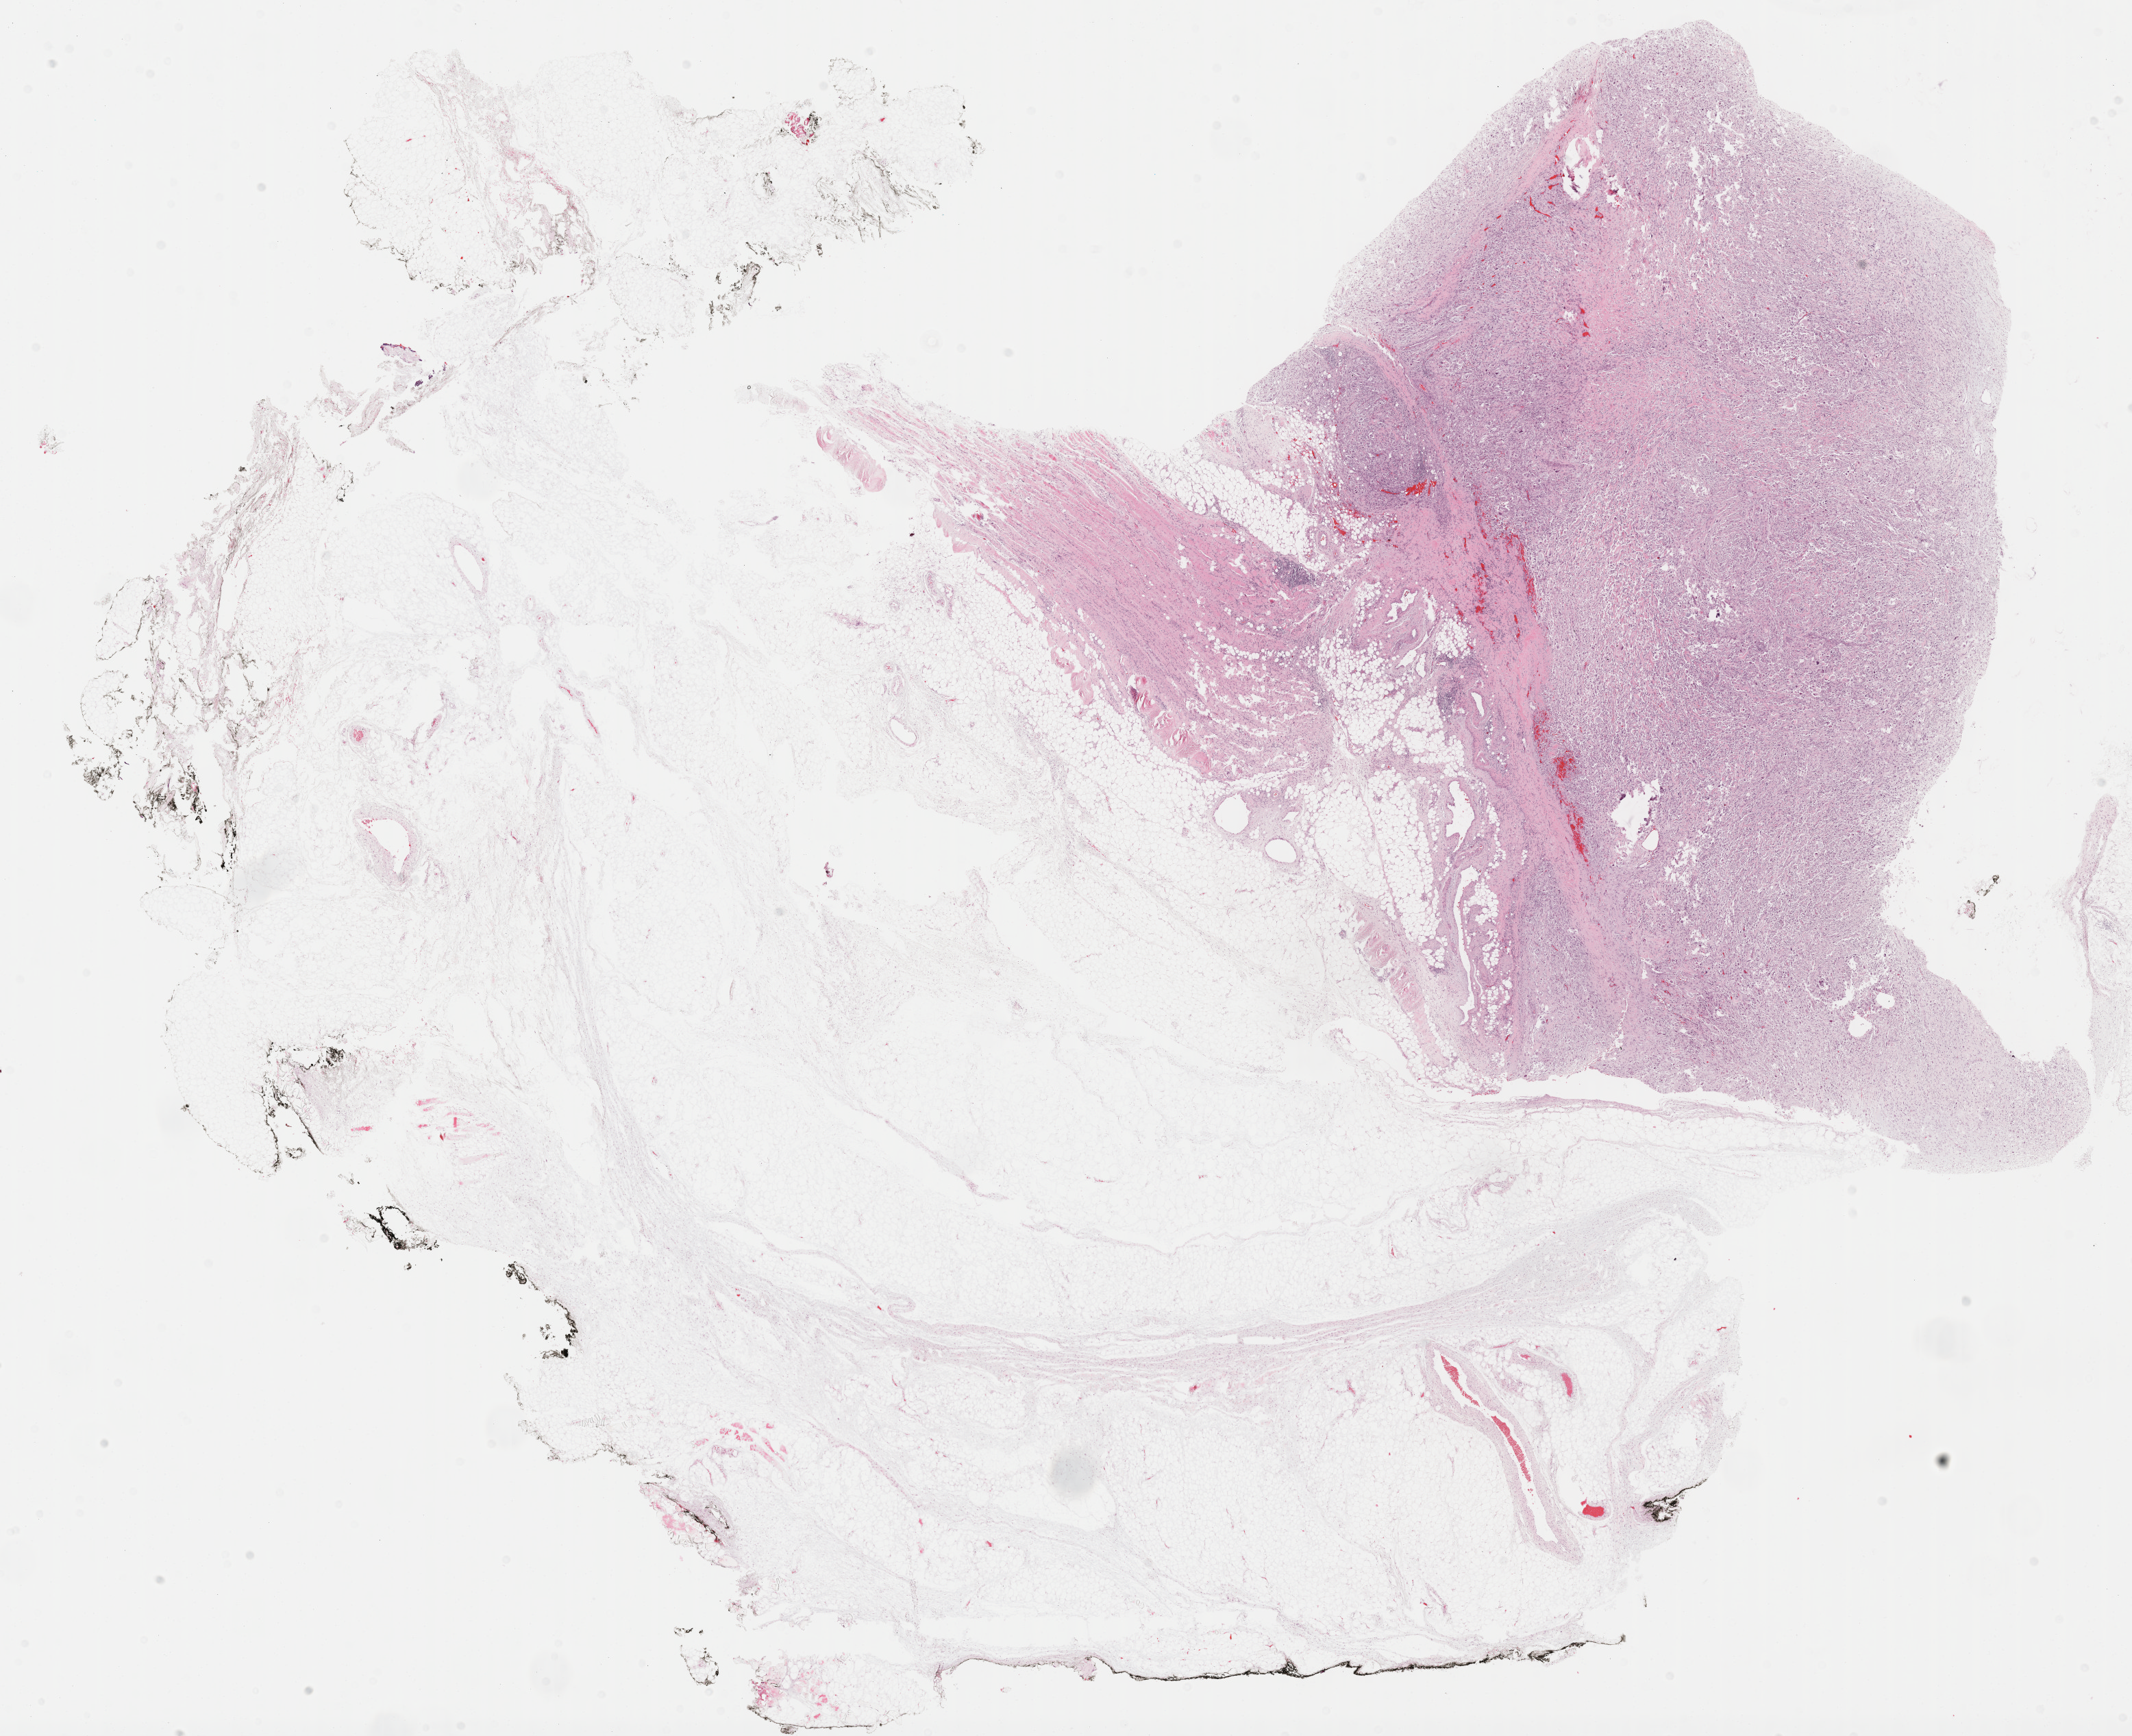
H&E whole-slide image — a low-resolution overview of the entire scanned area, about 25.2 x 20.5 mm (from a 40x scan); formalin-fixed paraffin-embedded (FFPE) diagnostic section; primary tumour sample from the connective, subcutaneous and other soft tissues. Male patient.
* pathologic diagnosis: Dedifferentiated liposarcoma (connective, subcutaneous and other soft tissues of thorax)